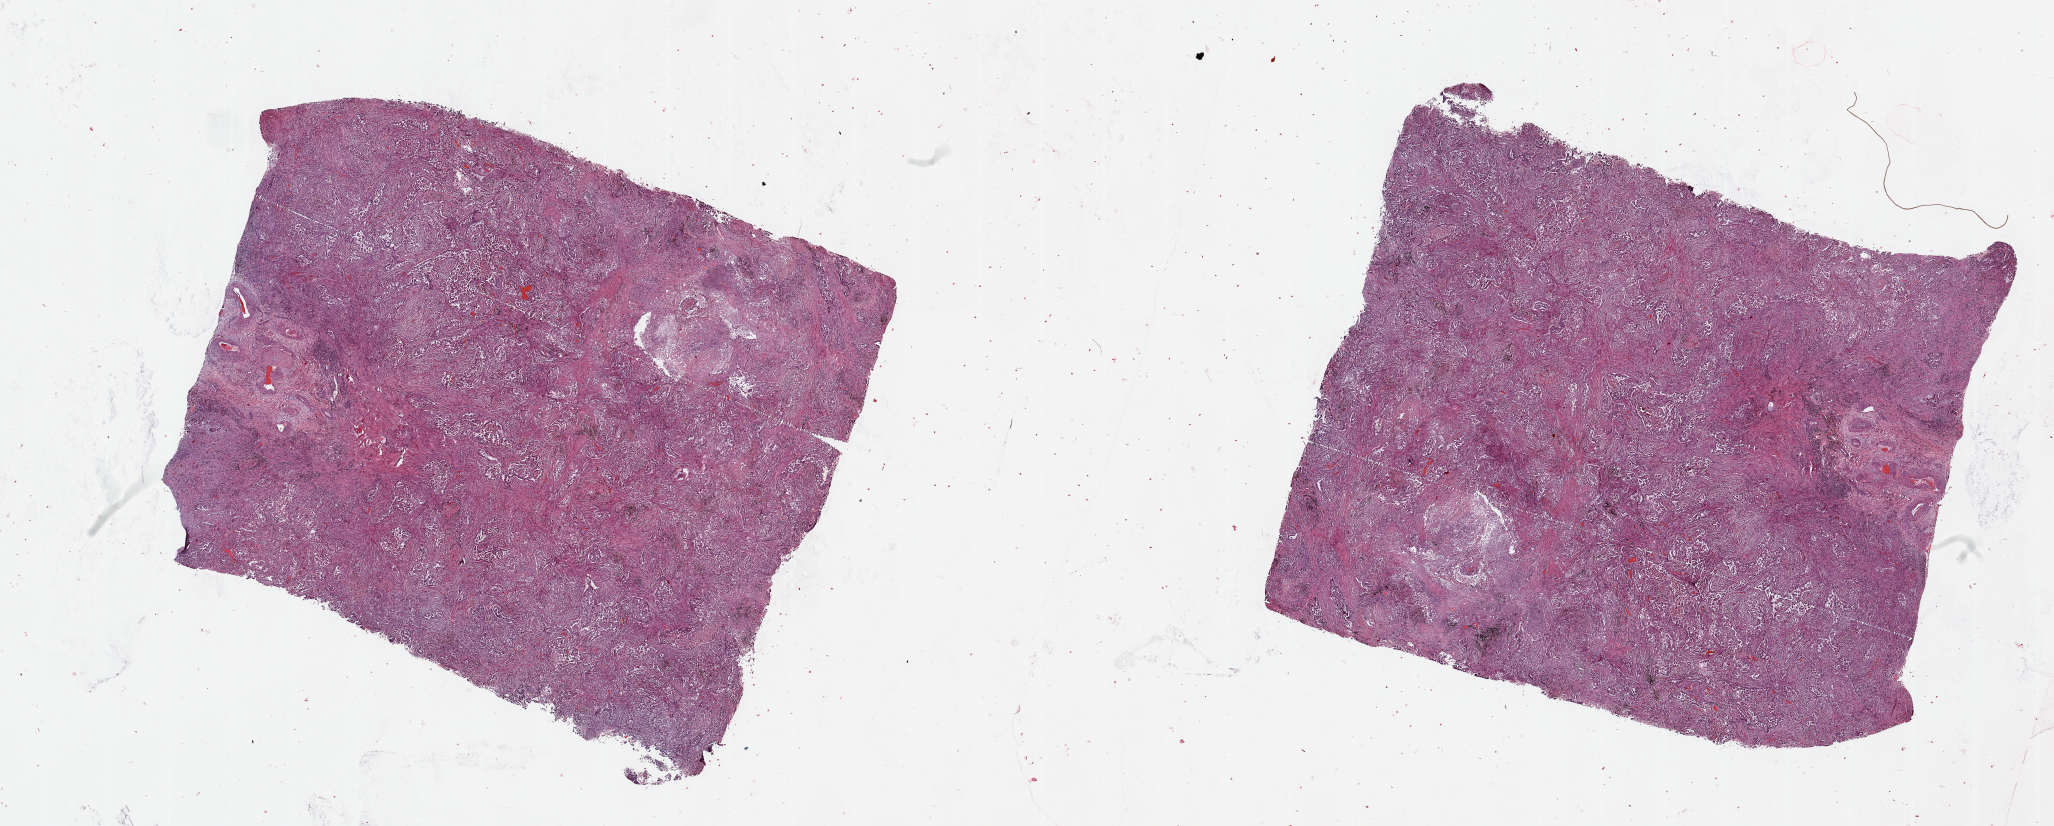
Digitized Hematoxylin and eosin (H&E) stained tissue section (whole slide), shown as a low-resolution overview of the whole scanned area (about 32.5 x 13.1 mm, acquisition: 20x scan), lung, tumour tissue. 59-year-old male patient. Histologic grade: G3 (poorly differentiated).
Primary tumour site (as recorded): right upper lobe. AJCC pathologic stage: IB. Histologic diagnosis: Adenocarcinoma, NOS.